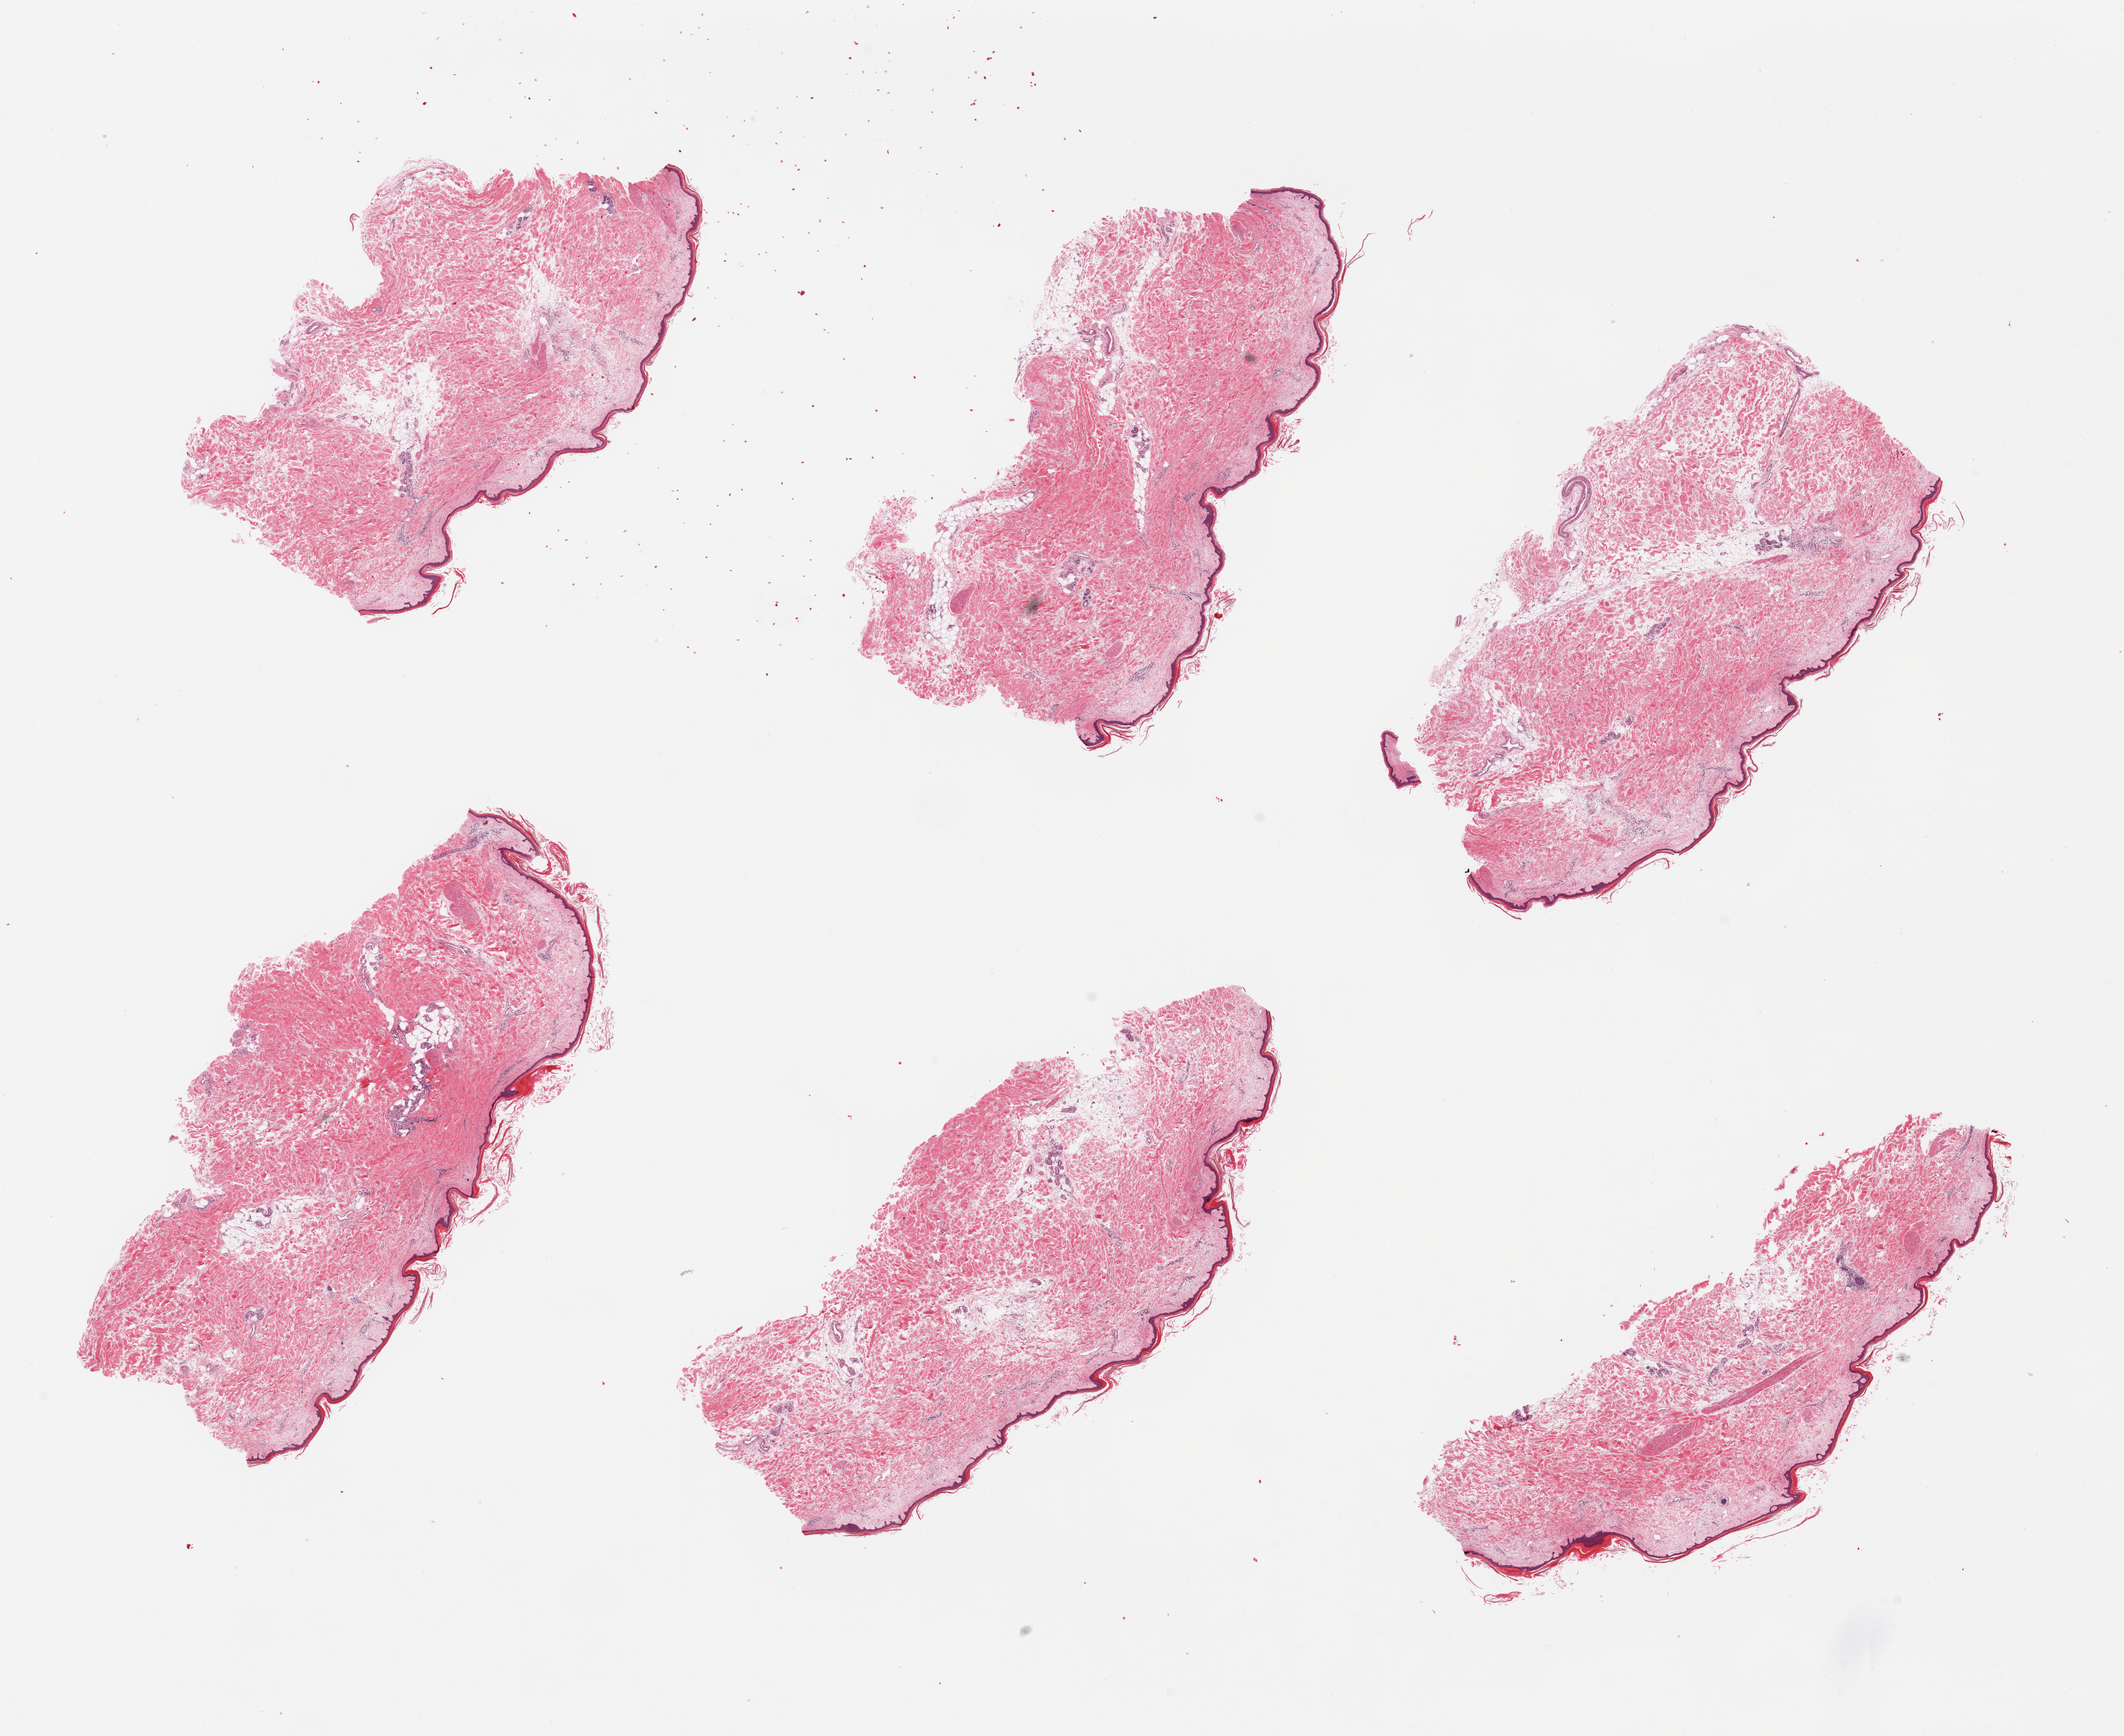
Whole-slide image, haematoxylin and eosin stain, whole scanned area (about 24.6 x 20.1 mm) shown as a low-resolution overview. PAXgene-fixed, paraffin-embedded tissue. Section of skin of lower leg (target tissue). Tissue donor sample. Donor: male.
Review note (as recorded): 6 pieces. well trimmed.